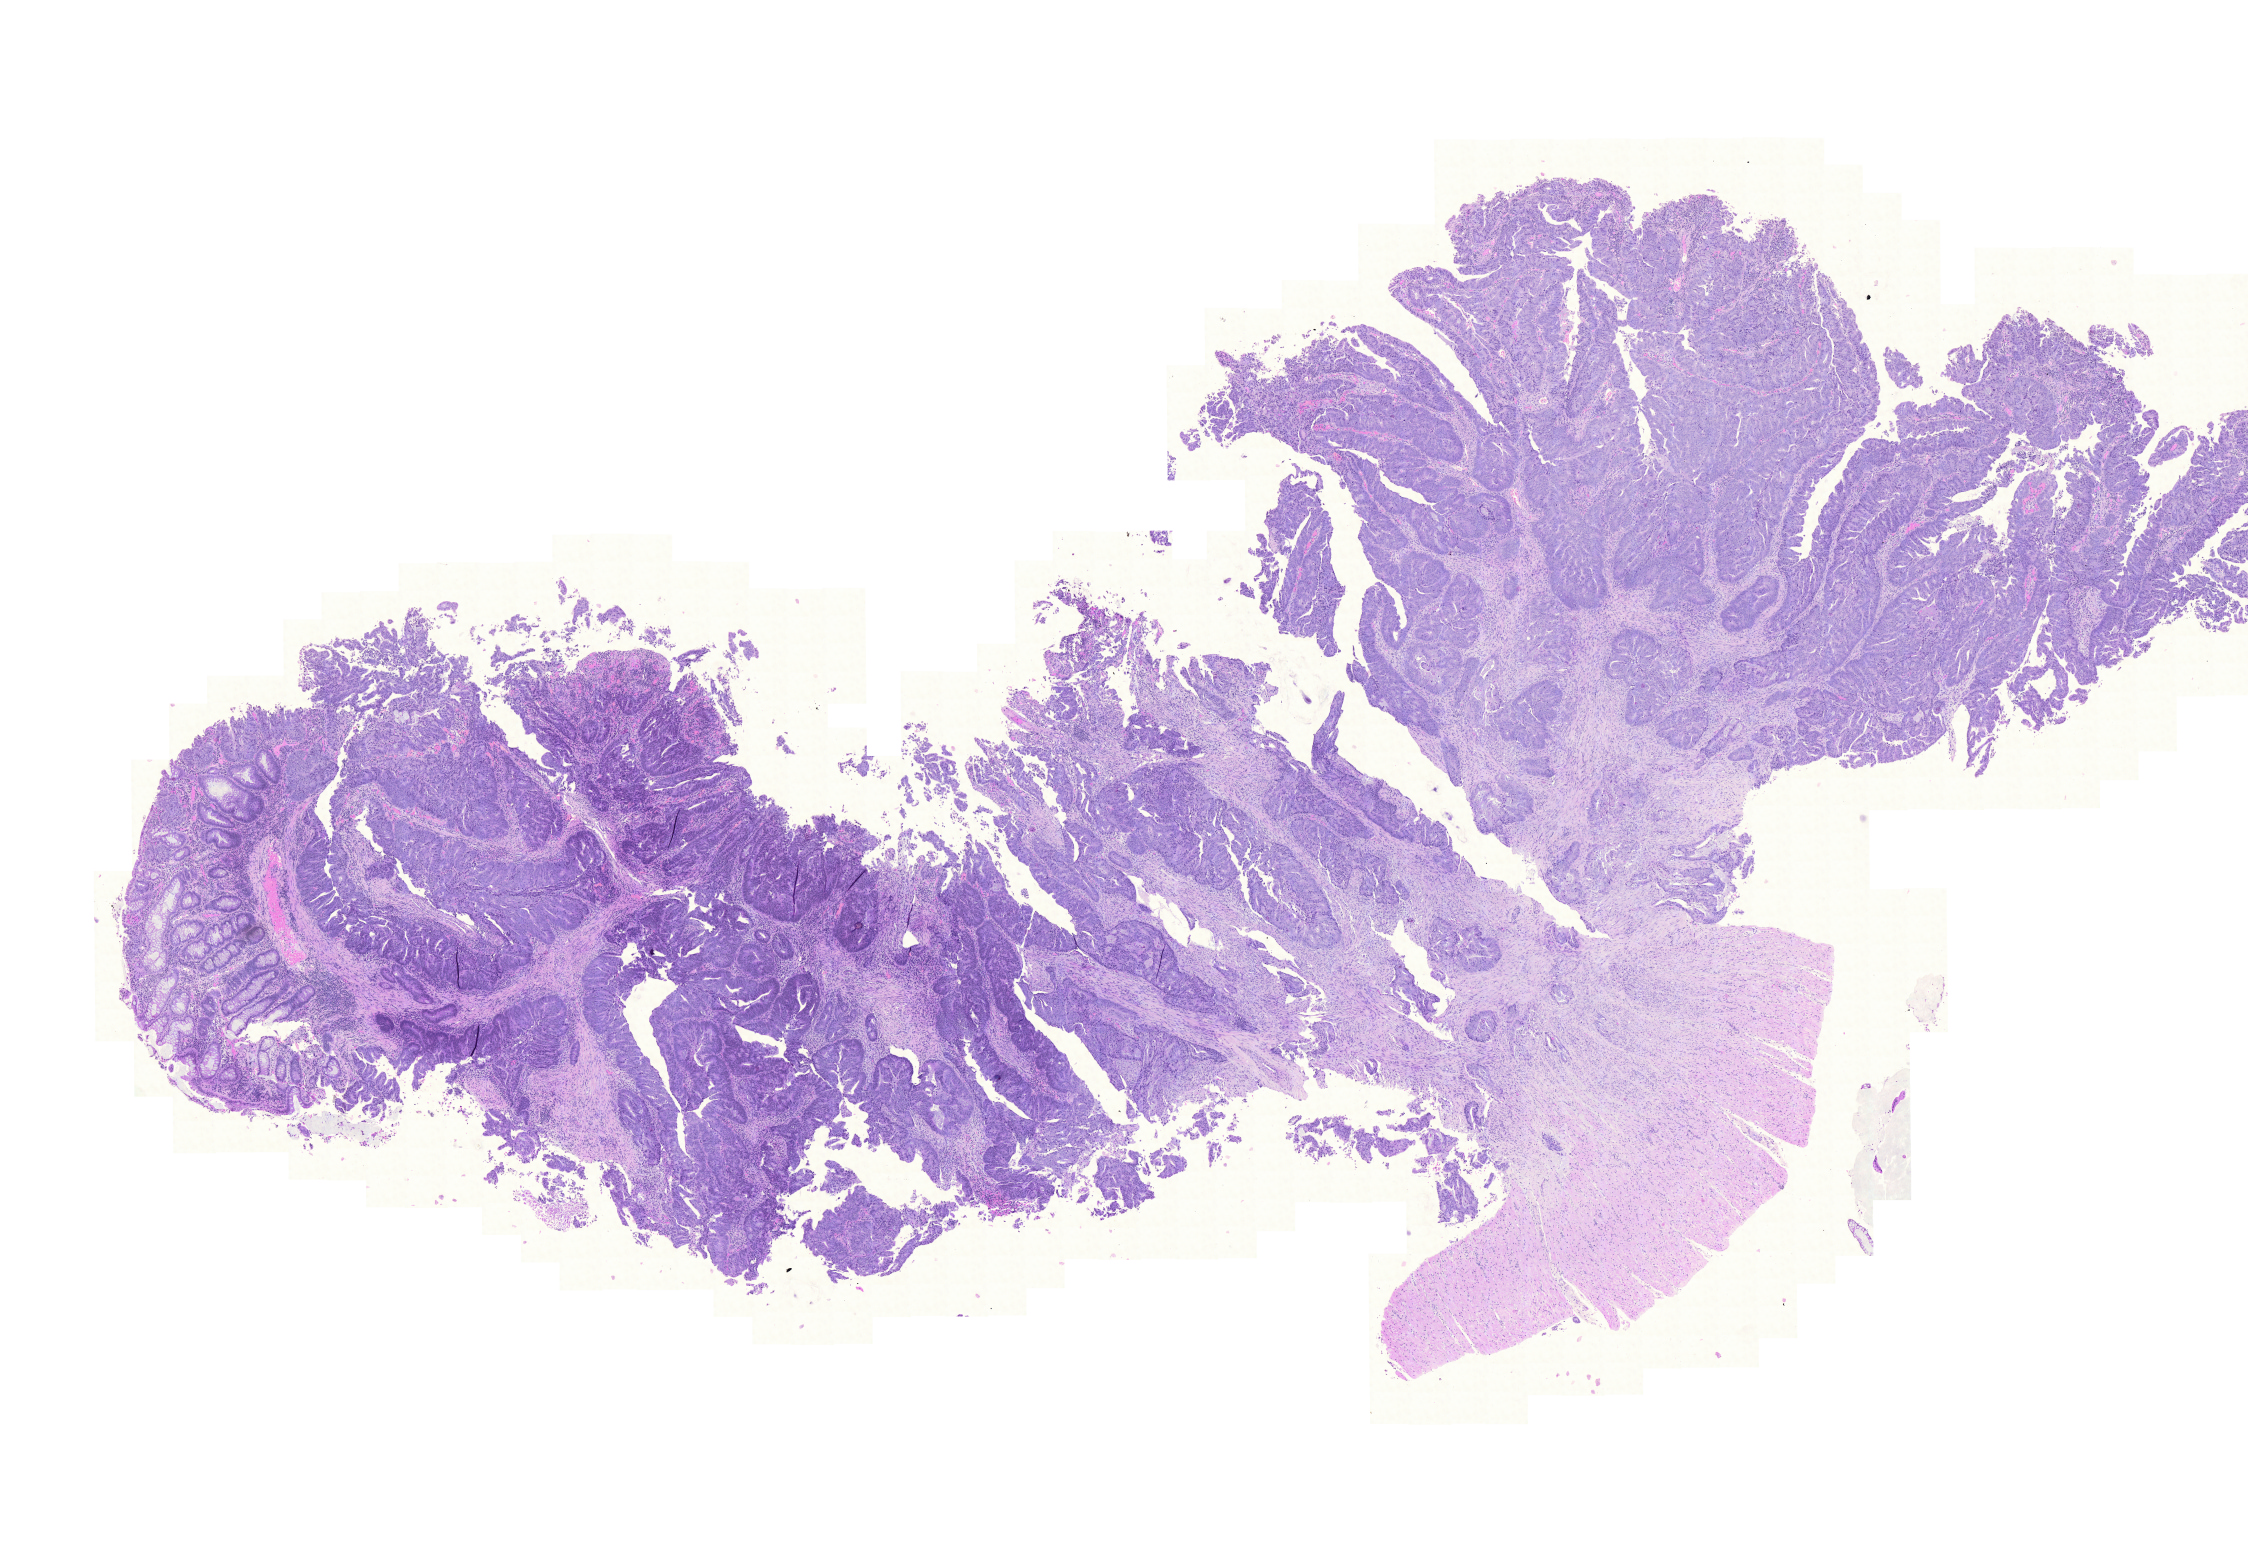
Whole-slide histology image, H&E, a low-resolution overview of the entire scanned area, about 16.7 x 11.5 mm (from a 20x scan), formalin-fixed paraffin-embedded (FFPE) diagnostic section, sample: primary tumour, rectum. Female patient; age at initial diagnosis 62 years.
Diagnosis: Adenocarcinoma, NOS. AJCC pathologic stage: IV. Lymph nodes positive (case pathology): 6 of 12 examined.